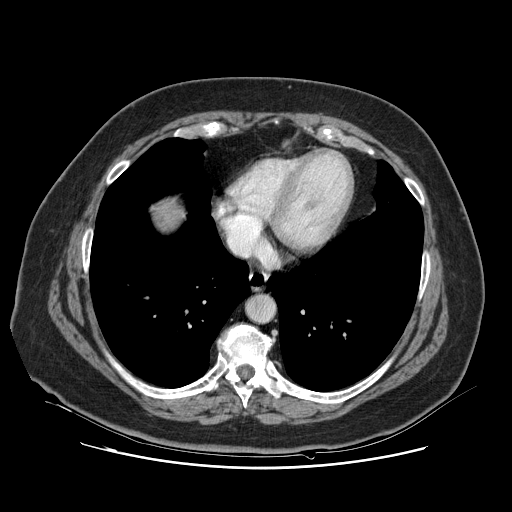
Contrast-enhanced abdominal CT, one axial slice; slice 123 of 132 in the series (ordered by position); 120 kVp; intravenous contrast given; soft-tissue window (W 400 / L 40 HU); 2.5 mm slice thickness; 512 × 512 image matrix, field of view 391 × 391 mm. Female patient, age 73 years. From the clinical record (not read from this slice): diagnosis: colorectal cancer liver metastases, imaged before liver resection.
Outlined on this slice (manually delineated by an expert):
- liver: bounding box <156,203,182,229> (left, top, right, bottom; pixels)
- planned liver remnant (the part of the liver to remain after resection): <157,203,183,229>